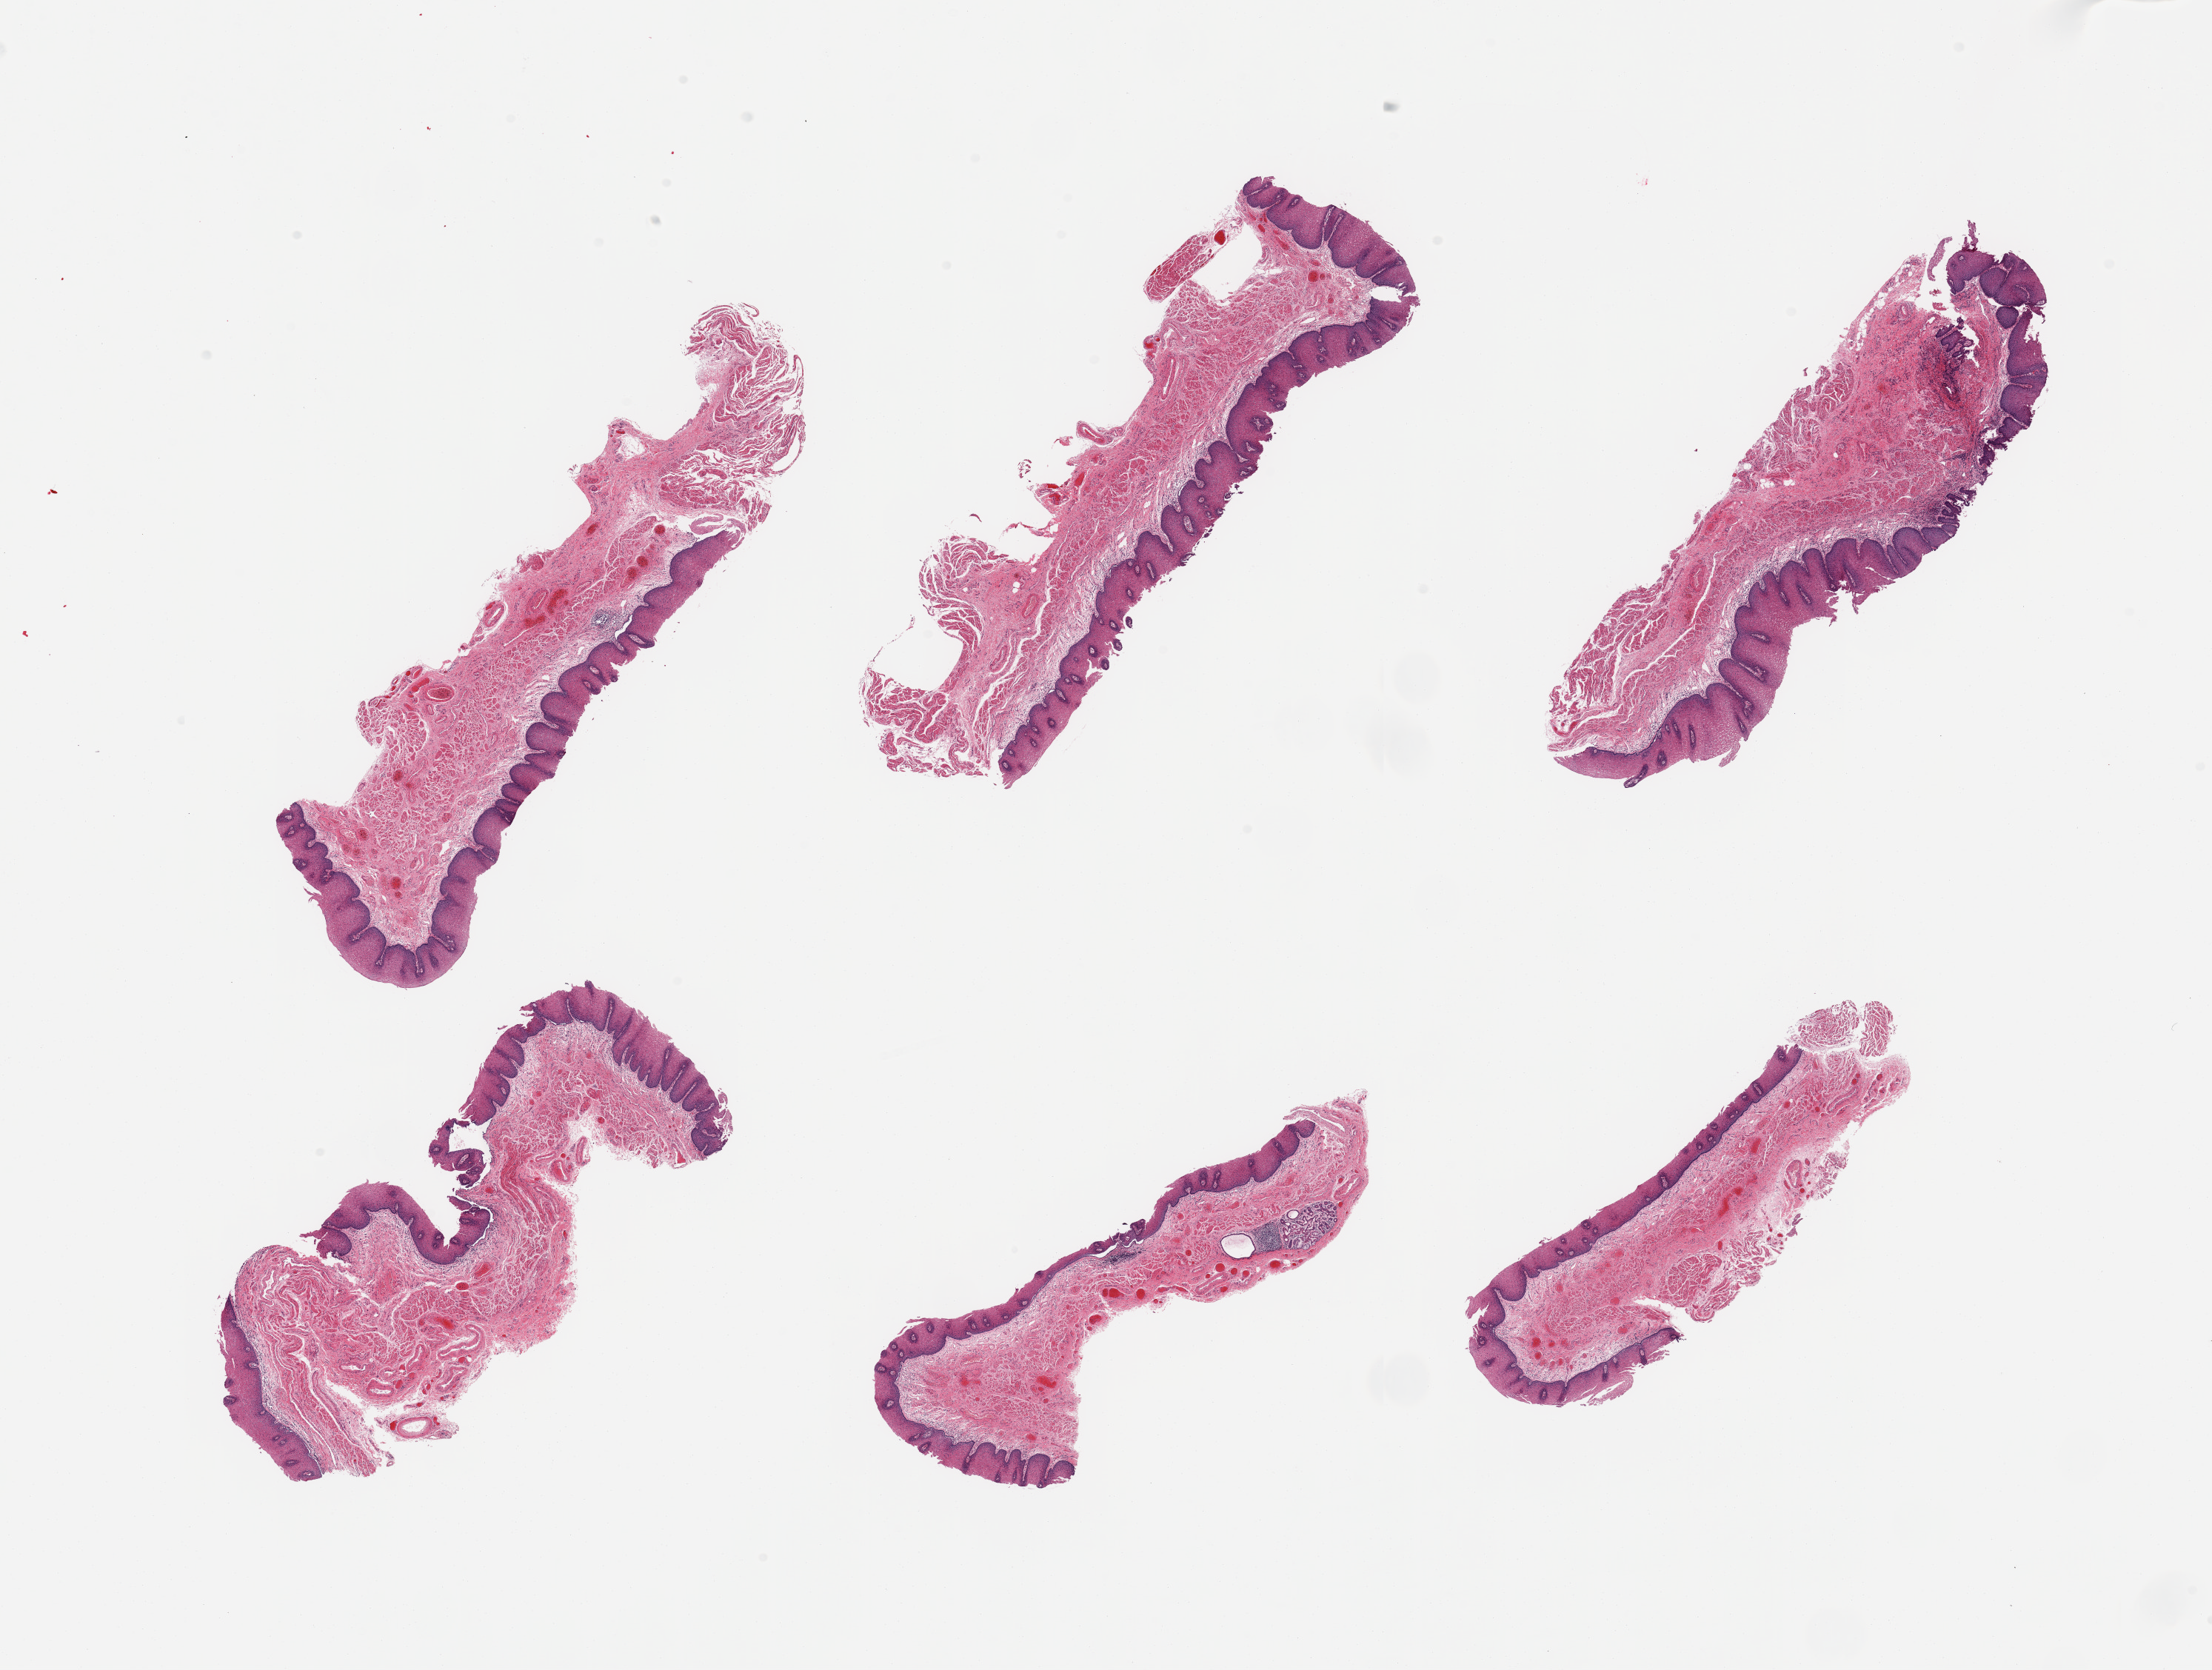
Whole-slide image, hematoxylin and eosin (H&E) stain, shown as a low-resolution overview of the whole scanned area (about 23.6 x 17.8 mm); PAXgene-fixed, paraffin-embedded tissue; section of gastroesophageal junction (target tissue); tissue donor sample. Donor: male.
Pathologist's review note for this sample: 6 pieces; mucosa sampled rather than muscularis propria.